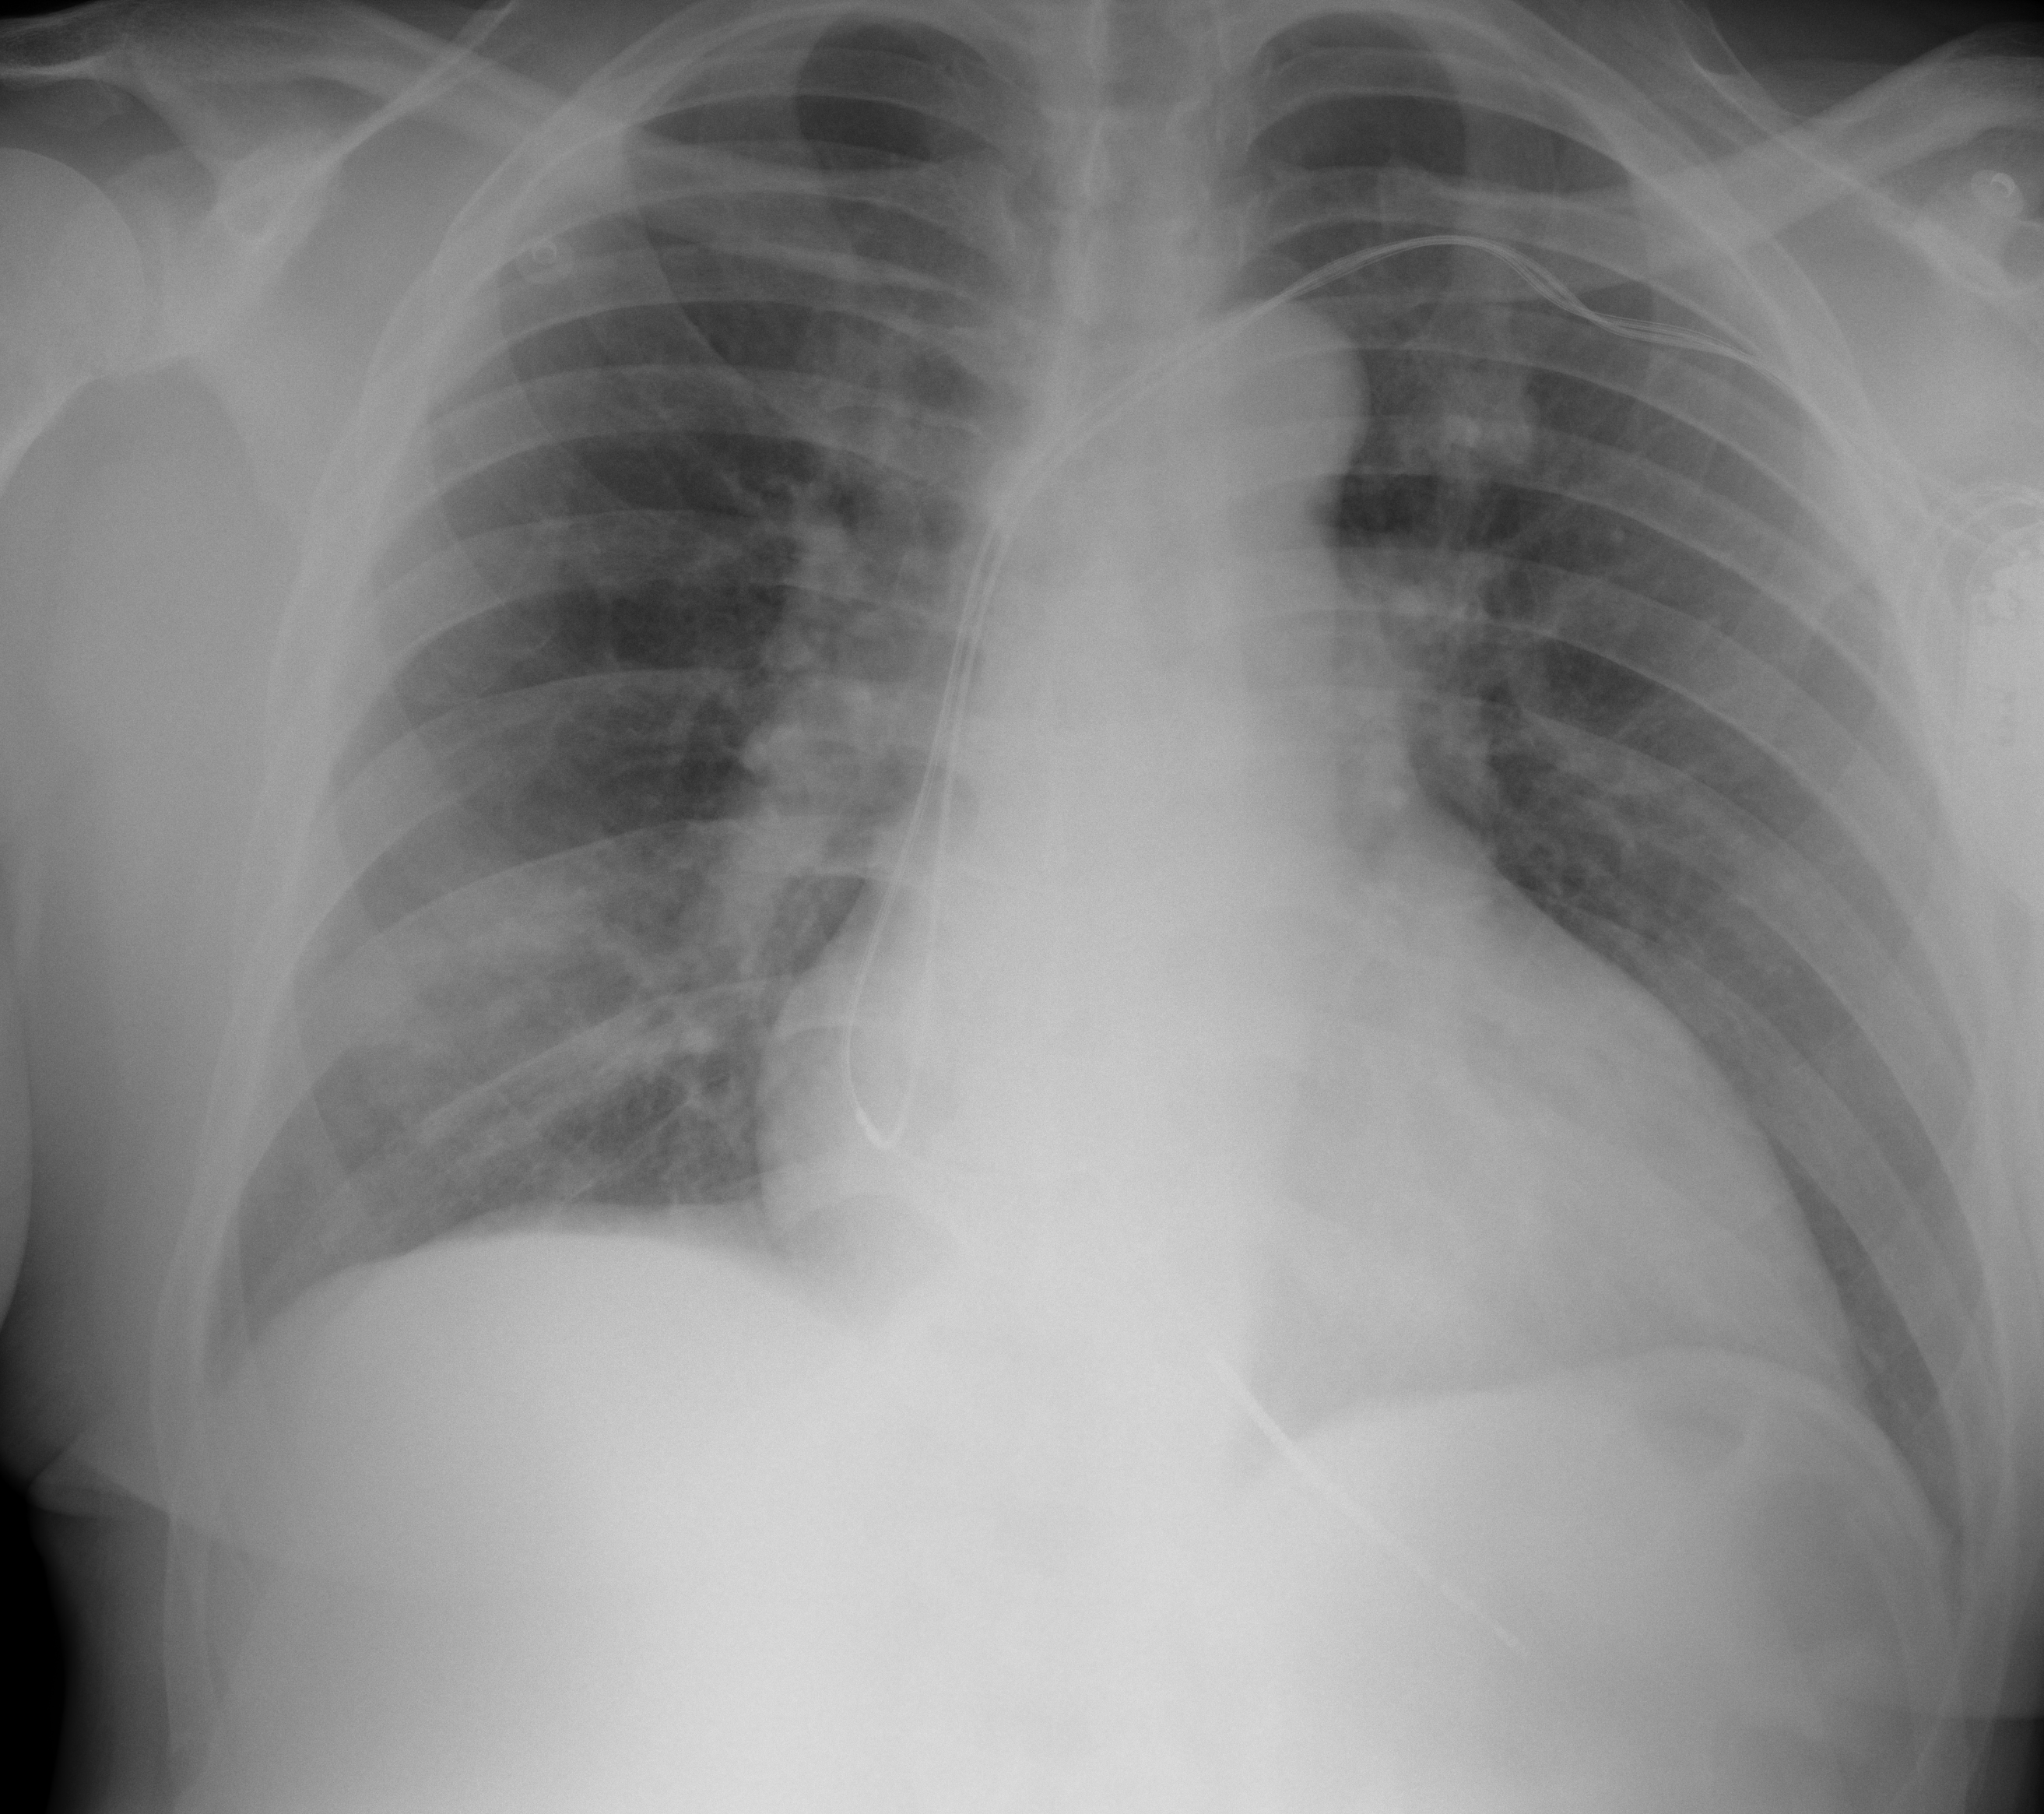
Portable chest radiograph, AP projection. Male patient, age 60 years; imaged 0 days after the COVID-19 diagnosis.
Radiologist's key findings for this exam: Focal area of consolidation within the right lower lobe.